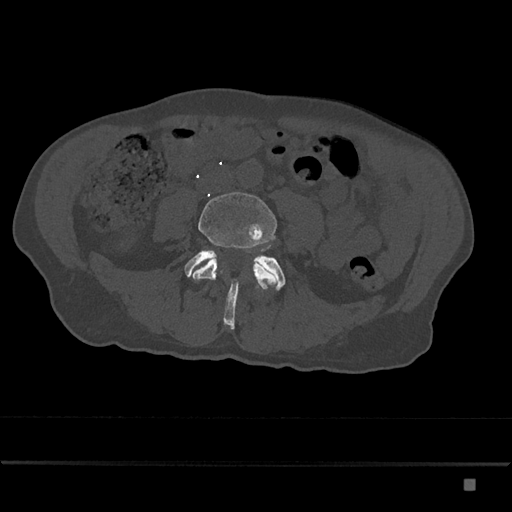
CT including the spine, one axial slice; 120 kVp; bone window (W 1800 / L 400 HU); 0.5 mm slice thickness; 512 × 512 image matrix, field of view 390 × 390 mm. Patient: male, 72 years. Case-level facts recorded for this patient, not image findings: primary cancer: prostate.
Structures marked on this image (semi-automatically segmented with operator editing):
- L4 vertebra: box from (x=190, y=192) to (x=277, y=290) px
- L5 vertebra: (x=184, y=250)–(x=286, y=330)